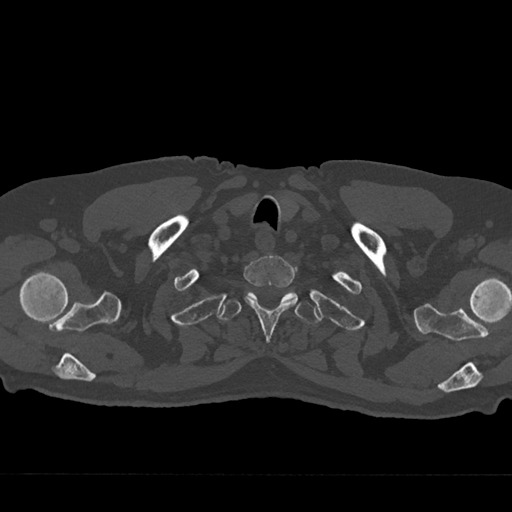
CT including the spine, one axial slice; position 641 of 797 along the scan axis; reconstruction kernel Br40s/3; bone window (W 1800 / L 400 HU); 0.5 mm slice thickness; 512 × 512 image matrix, field of view 377 × 377 mm. Patient: male, 75 years. From the clinical record (not read from this slice): primary cancer: renal; vertebrae with lytic lesions (as recorded): T4.
Structures marked on this image (semi-automatically segmented with operator editing):
- T1 vertebra: box from (x=244, y=255) to (x=298, y=342) px
- T2 vertebra: (x=218, y=291)–(x=320, y=324)